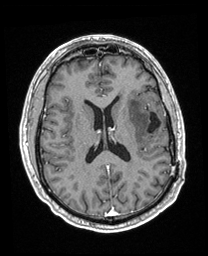
Brain MRI from a brain-tumour surgery series, one axial slice; position 95 of 208 along the scan axis; T1-weighted post-contrast; 1 mm slice thickness; 208 × 256 image matrix, field of view 211 × 260 mm. Case-level facts recorded for this patient, not image findings: histopathology: Astrocytoma; WHO grade: 3; IDH mutation: yes.
Structures marked on this image (expert manual segmentation):
- previous resection cavity: bounding box <147,112,161,134> (left, top, right, bottom; pixels)